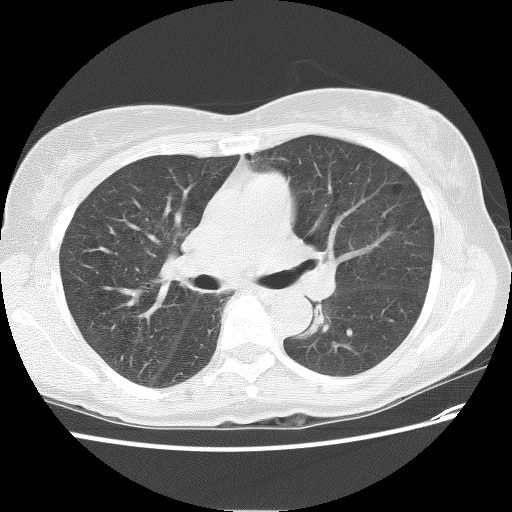
Chest CT (low-dose screening protocol), one axial image; baseline annual screen; lung window (W 1500 / L -600 HU); 2.5 mm slice thickness; lung (sharp) reconstruction kernel (BONE); slice 46 of 118 in the series. Female participant, aged 62 years at enrolment.
• Expert-annotated lung lesion, box from (x=287, y=297) to (x=345, y=343) px.
• No non-calcified nodule or mass ≥4 mm was recorded by the screening reader at this exam.
• Official screen result: negative screen, minor abnormalities not suspicious for lung cancer.
• Lung cancer was diagnosed 898 days after this screen: squamous cell carcinoma, NOS, left lower lobe, stage IIIB (AJCC 6th edition), 31 mm at pathology.